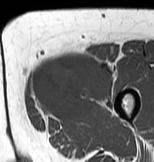
MRI of an extremity soft-tissue mass, one axial slice. Position 23 of 83 along the scan axis. MR volume resampled by the dataset authors to the PET/CT grid (not the native acquisition matrix). 3.27 mm slice thickness. 154 × 162 image matrix, field of view 150 × 158 mm. Female patient. From the clinical record (not read from this slice): histological type: myxofibrosarcoma; grade: intermediate; site of the primary tumour: left thigh.
Structures marked on this image (expert contour drawn on MRI and transferred to this co-registered scan by the dataset authors):
- gross tumour volume including surrounding oedema: bounding box <30,50,116,124> (left, top, right, bottom; pixels)
- gross tumour volume (mass): <31,54,114,119>